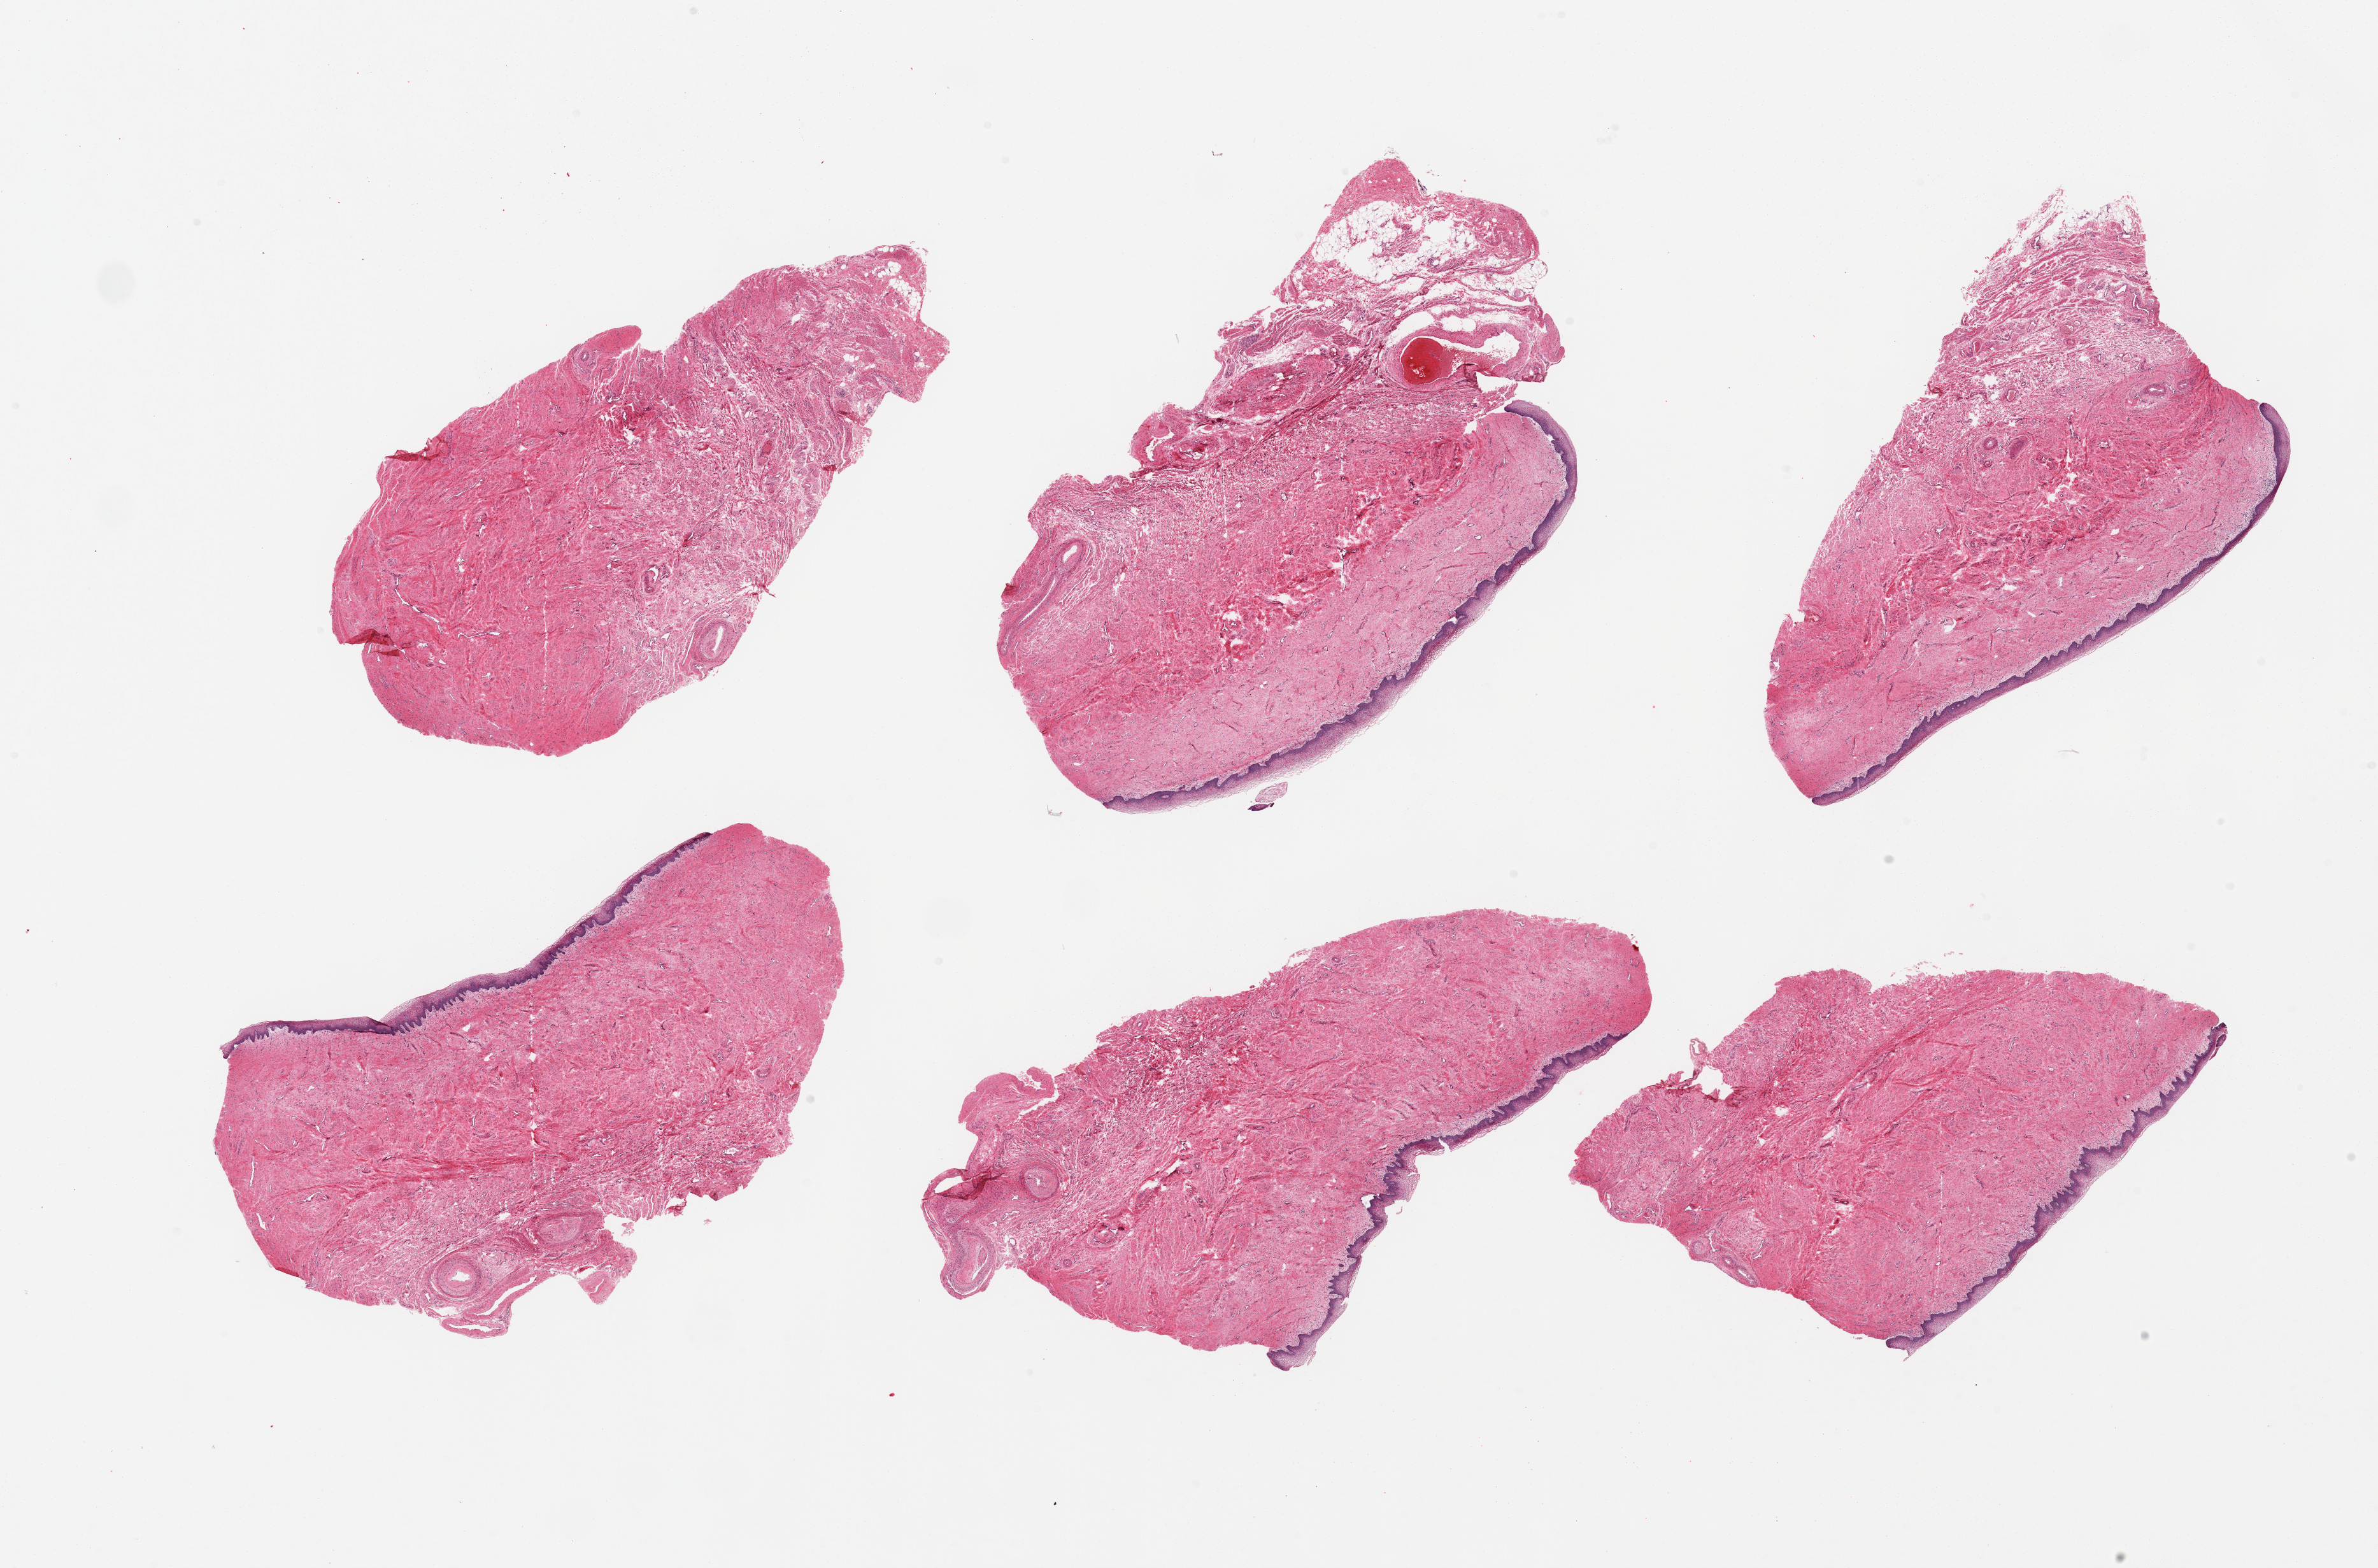
Whole-slide image, haematoxylin and eosin stain, shown as a low-resolution overview of the whole scanned area (about 29.5 x 19.5 mm, from a 20x scan), PAXgene-fixed, paraffin-embedded tissue, sampled site (target tissue): vagina, donor tissue sample. Donor sex: female.
- review note (as recorded): 6 pieces; 1 has no epithelium (in this cut)